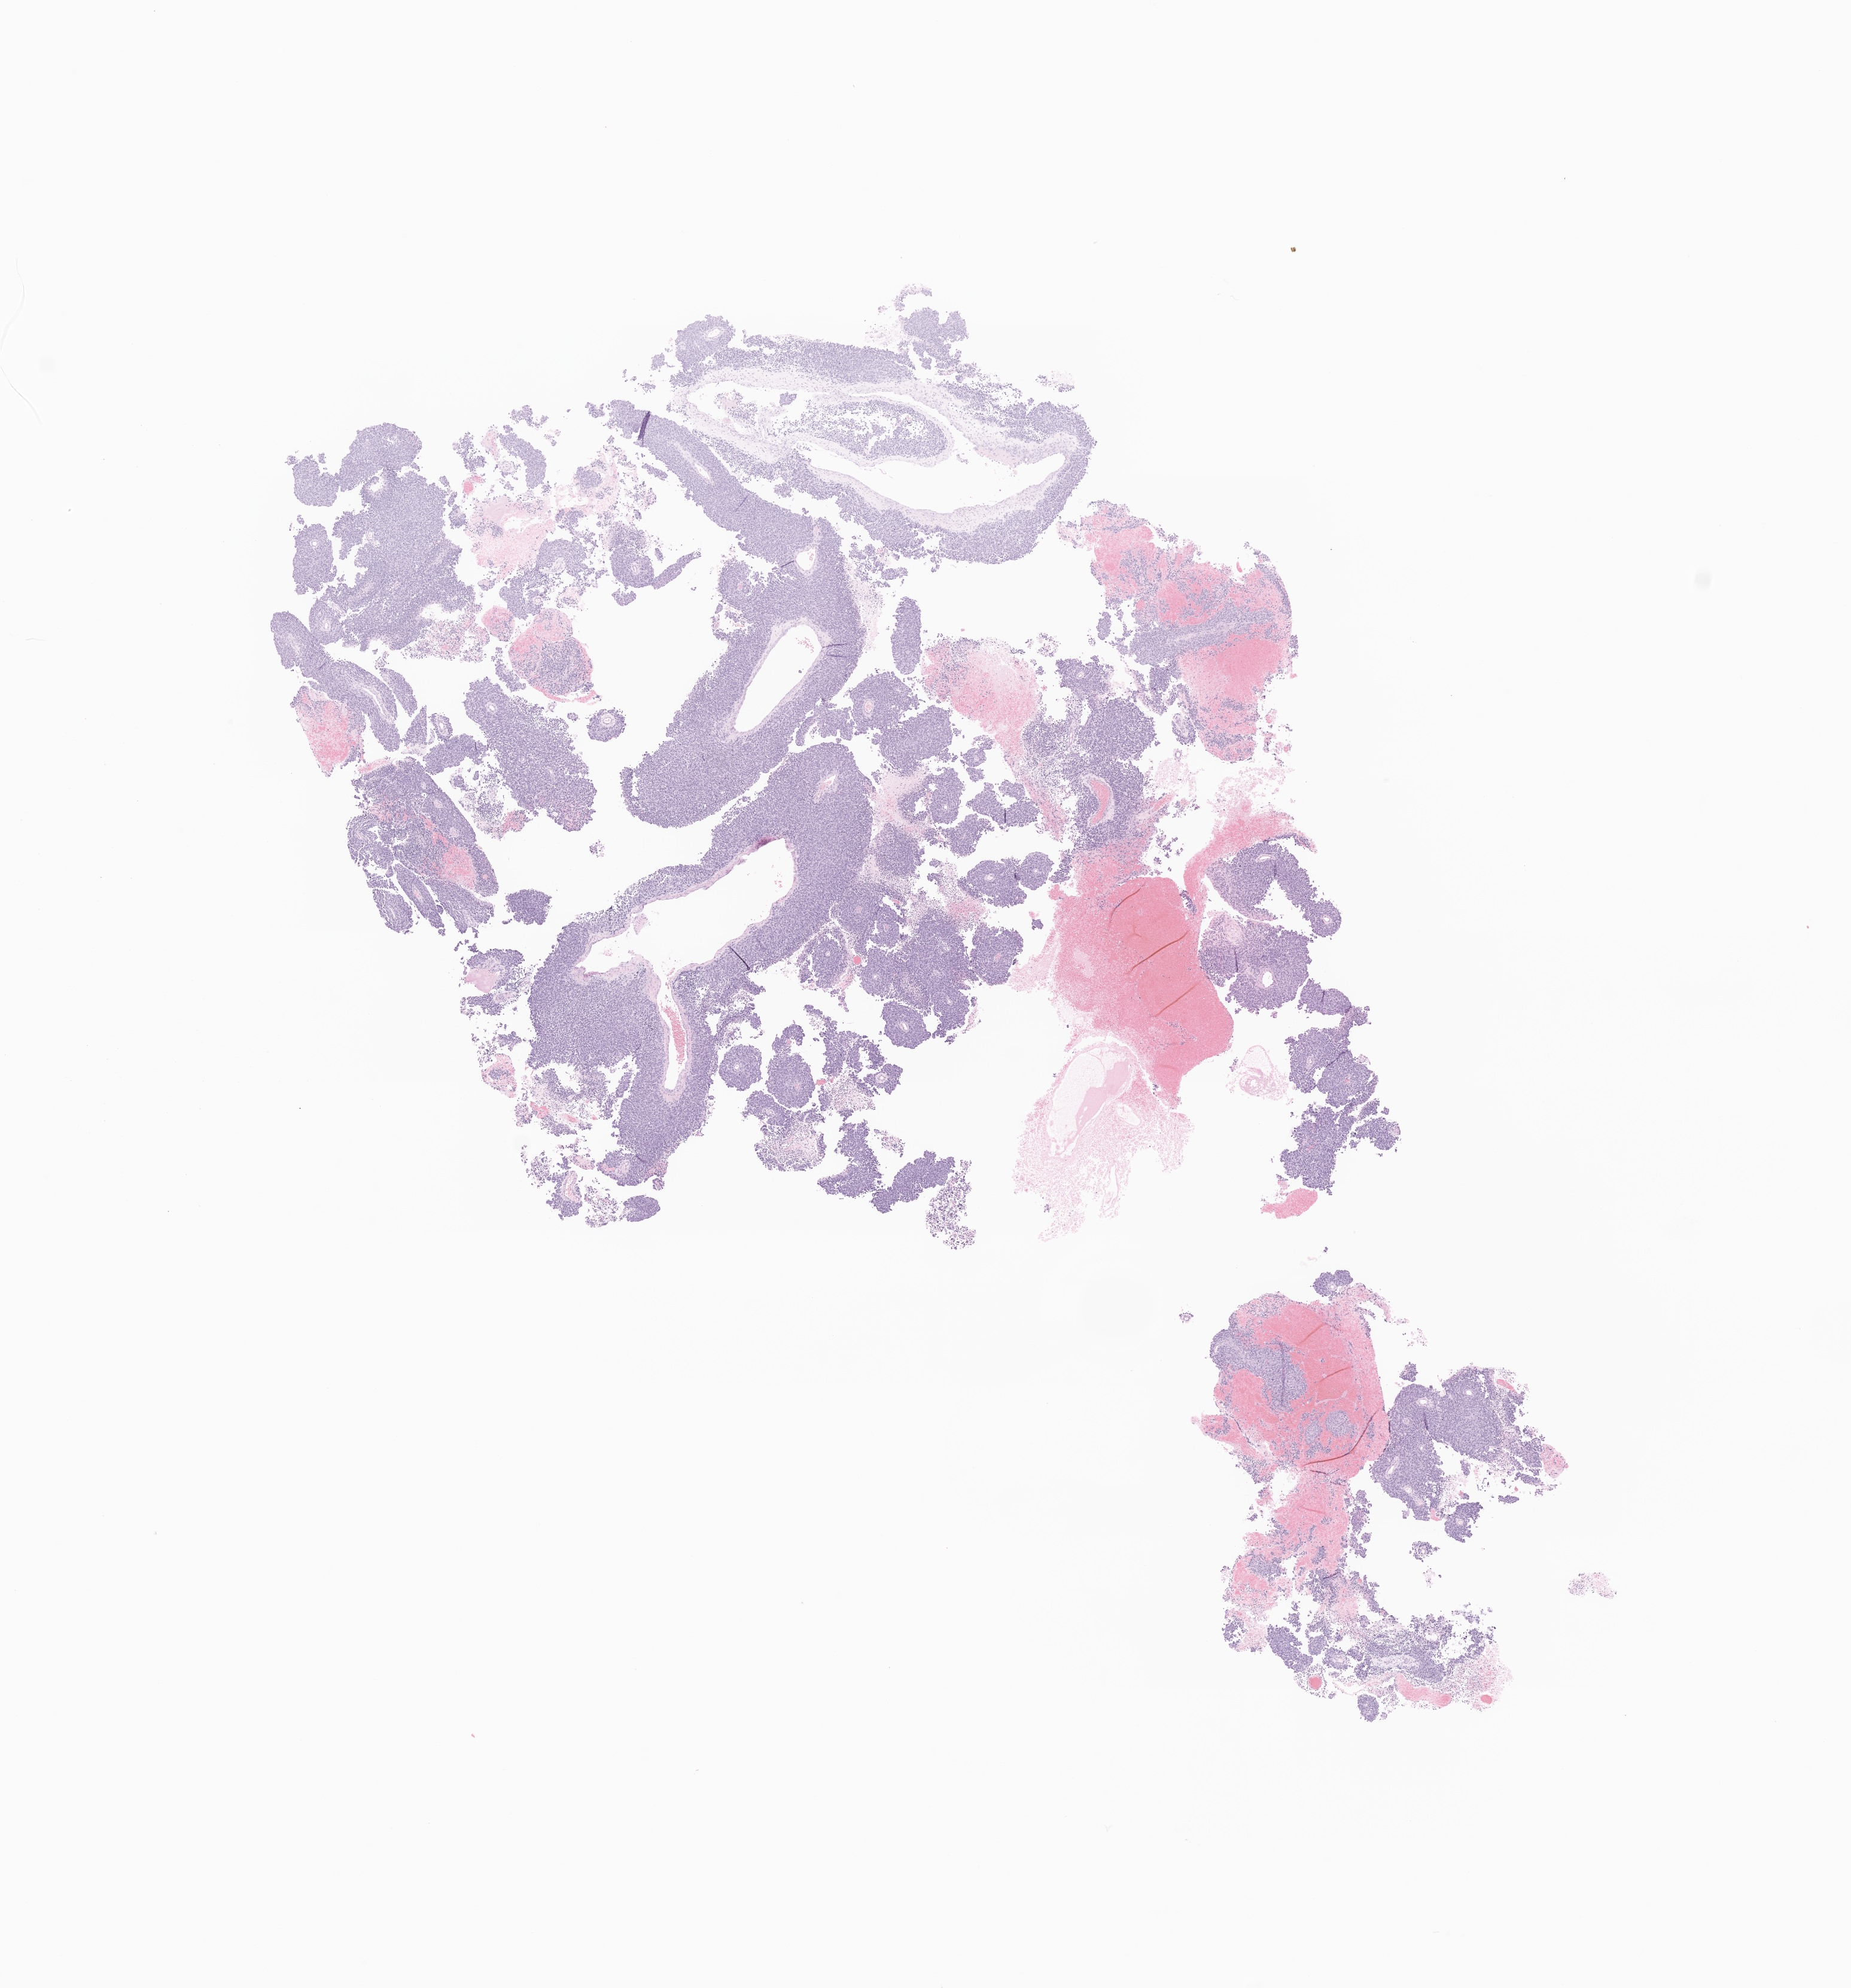
H&E whole-slide image of tumor tissue from the brain, a low-resolution overview of the entire scanned area, about 13.0 x 14.0 mm; FFPE section. Patient: female, age 88 months.
- diagnosis: Glioma, malignant